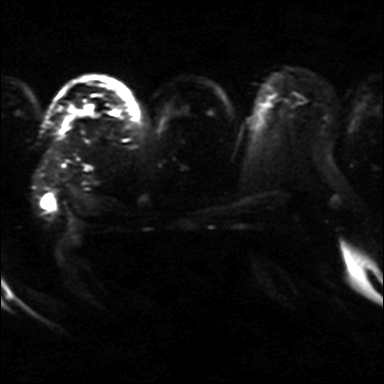
Breast MRI, one axial slice. Position 26 of 36 along the scan axis. Diffusion-weighted series; image 2 of 4 stored at this slice position (different b-values; order by instance number). 3 T. 4 mm slice thickness. 384 × 384 image matrix, field of view 320 × 320 mm. Female patient.
Structures marked on this image (expert manual segmentation):
- tumour on diffusion-weighted imaging: bounding box [x1, y1, x2, y2] px = [82, 103, 94, 115]